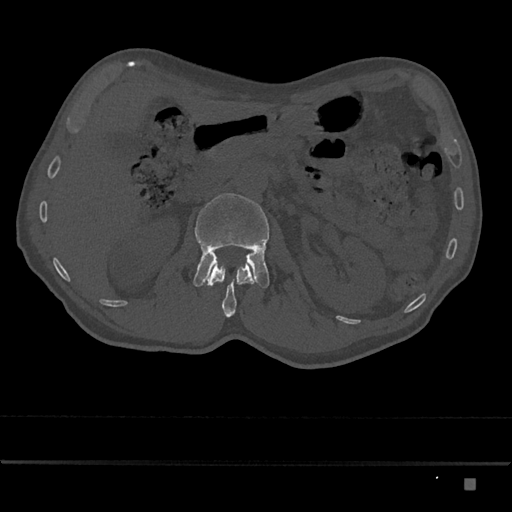
CT including the spine, one axial slice. Position 506 of 797 along the scan axis. Reconstruction kernel Br40s/3. 120 kVp. Bone window (W 1800 / L 400 HU). 512 × 512 image matrix, field of view 390 × 390 mm. Patient: male, 72 years. From the clinical record (not read from this slice): primary cancer: prostate.
Structures marked on this image (semi-automatically segmented with operator editing):
- L1 vertebra: box from (x=206, y=262) to (x=256, y=318) px
- L2 vertebra: (x=193, y=193)–(x=270, y=288)